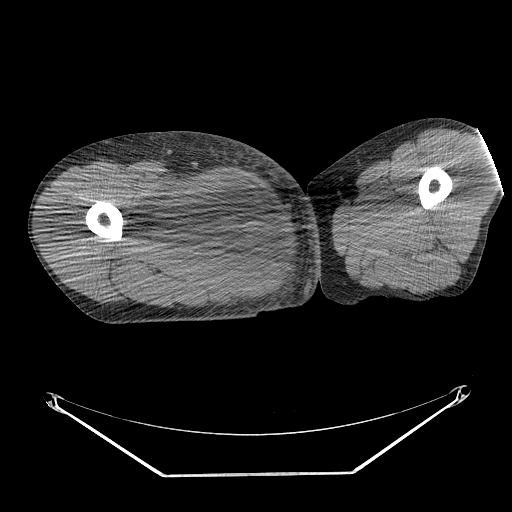
CT of an extremity soft-tissue mass (from a PET/CT study), one axial slice; position 249 of 311 along the scan axis; 140 kVp; soft-tissue window (W 400 / L 40 HU); 3.75 mm slice thickness; 512 × 512 image matrix, field of view 500 × 500 mm. Male patient. From the clinical record (not read from this slice): histological type: undifferentiated - pleiomorphic; grade: high; site of the primary tumour: right thigh.
Structures marked on this image (expert contour drawn on MRI and transferred to this co-registered scan by the dataset authors):
- gross tumour volume including surrounding oedema: bounding box [x1, y1, x2, y2] px = [132, 174, 252, 264]
- gross tumour volume (mass): [155, 174, 252, 264]